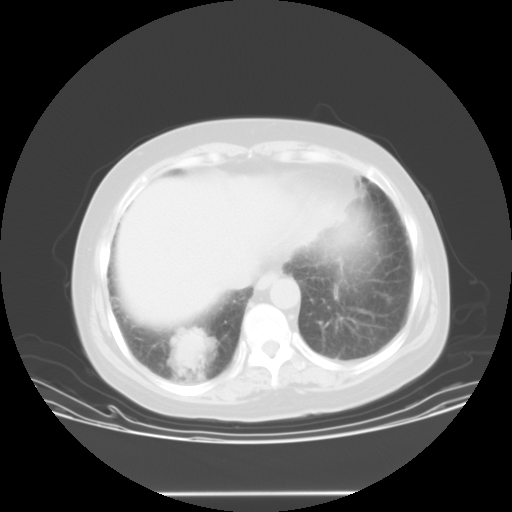
Chest CT, one axial slice. Slice 4 of 23 in the series (ordered by position). Lung window (W 1500 / L -600 HU). 10 mm slice thickness. 512 × 512 image matrix. Female patient, age 55 years. Case-level facts recorded for this patient, not image findings: clinical TNM (as recorded): T2 N0 M1b.
Structures marked on this image (bounding box drawn by a radiologist):
- lung tumour (recorded histology: squamous cell carcinoma): box from (x=165, y=321) to (x=218, y=385) px